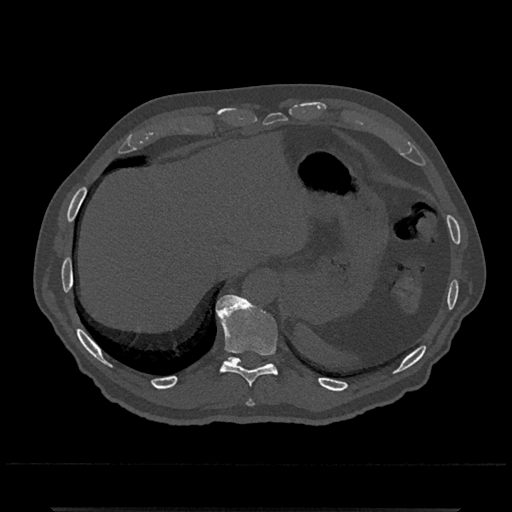
CT including the spine, one axial slice. Position 546 of 797 along the scan axis. 120 kVp. Bone window (W 1800 / L 400 HU). 512 × 512 image matrix, field of view 393 × 393 mm. Patient: male, 67 years. From the clinical record (not read from this slice): primary cancer: prostate.
Annotated regions visible in this slice (semi-automatically segmented with operator editing):
- T10 vertebra: box from (x=210, y=294) to (x=278, y=387) px
- T11 vertebra: (x=227, y=356)–(x=269, y=366)
- T9 vertebra: (x=247, y=400)–(x=254, y=407)